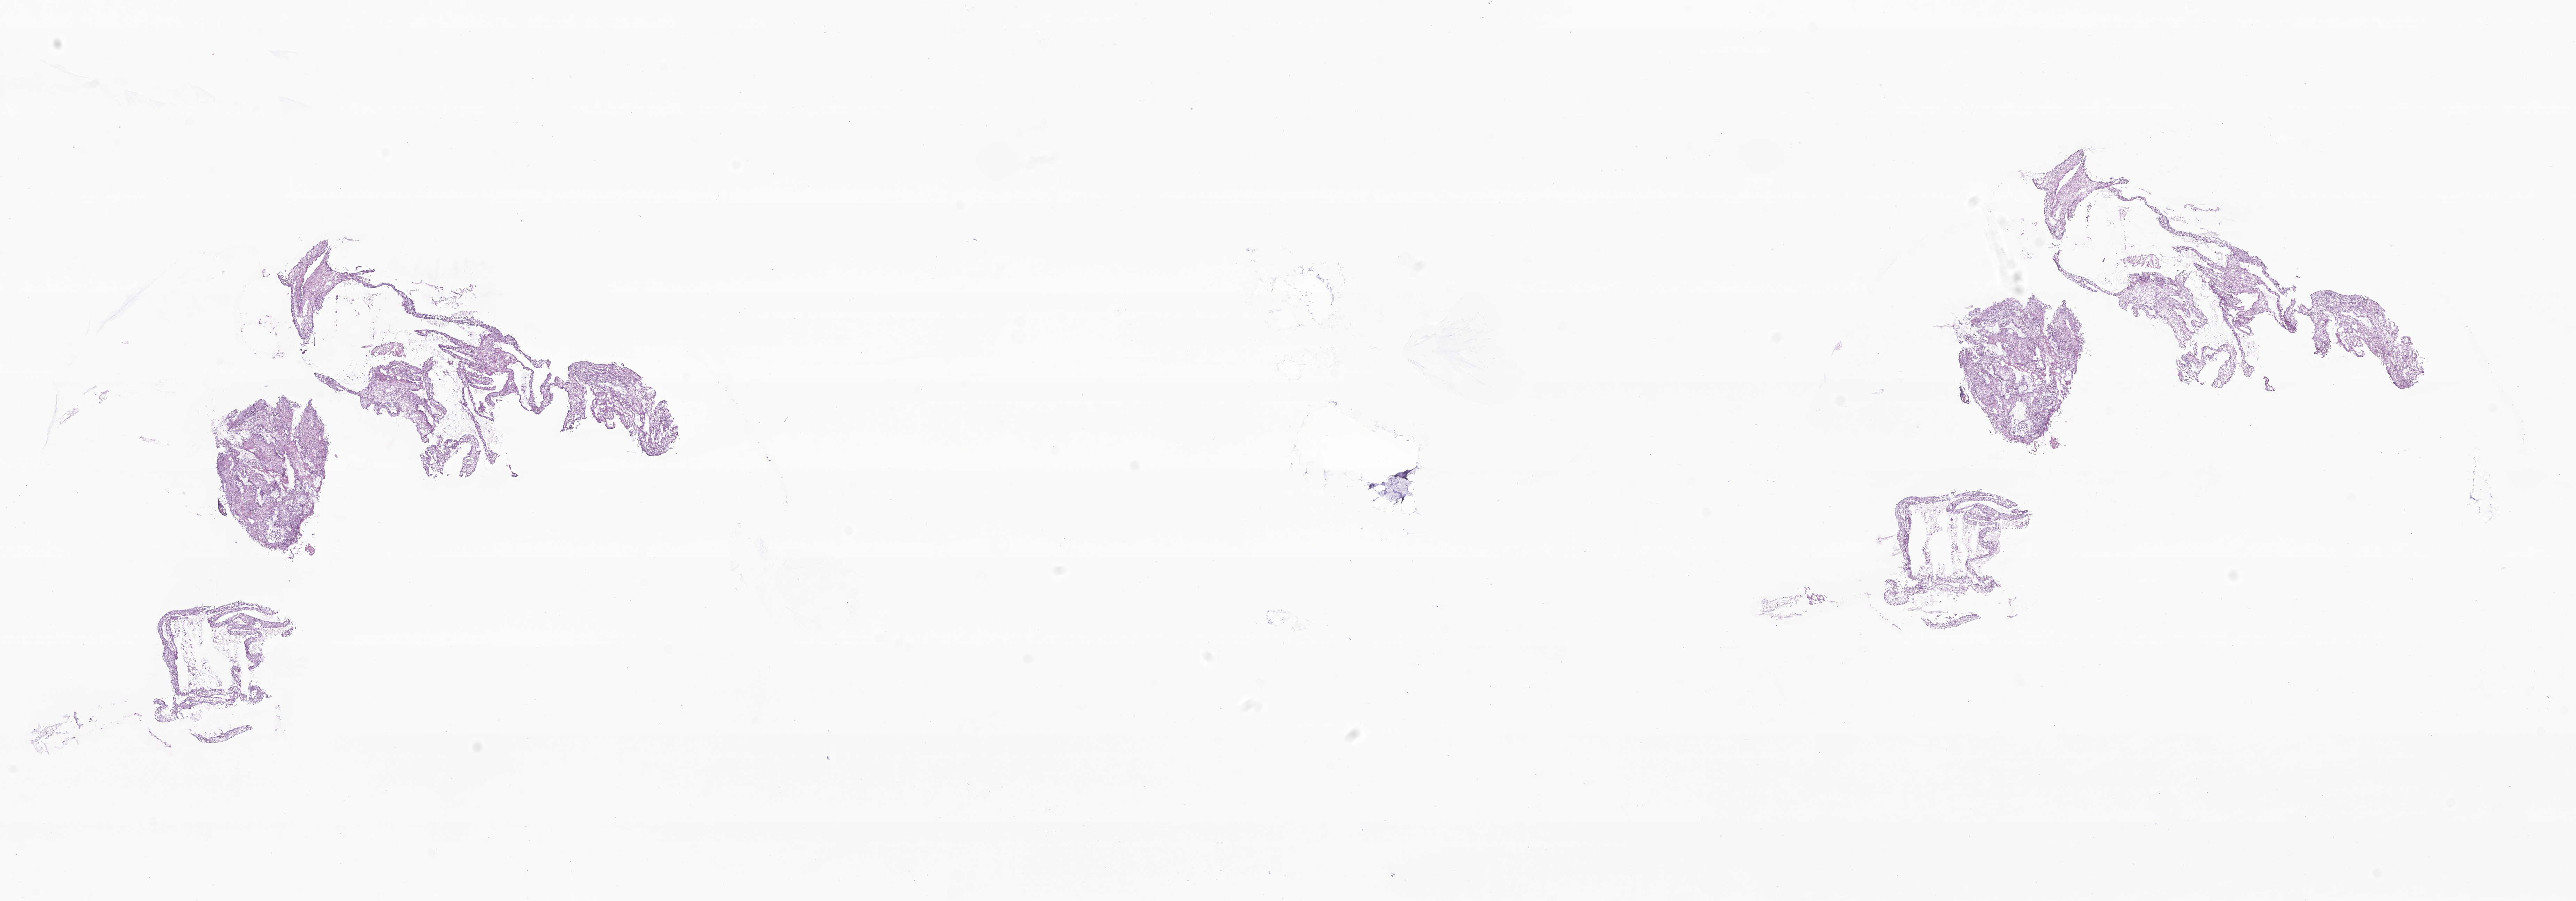
Haematoxylin and eosin whole-slide image of tumor tissue from the lower lobe of lung — low-resolution overview of the scanned area, about 31.2 x 10.9 mm, frozen section. Patient: male, age 77 days.
Diagnosis: Pleuropulmonary blastoma. Tissue or organ of origin (case record): lower lobe, lung.